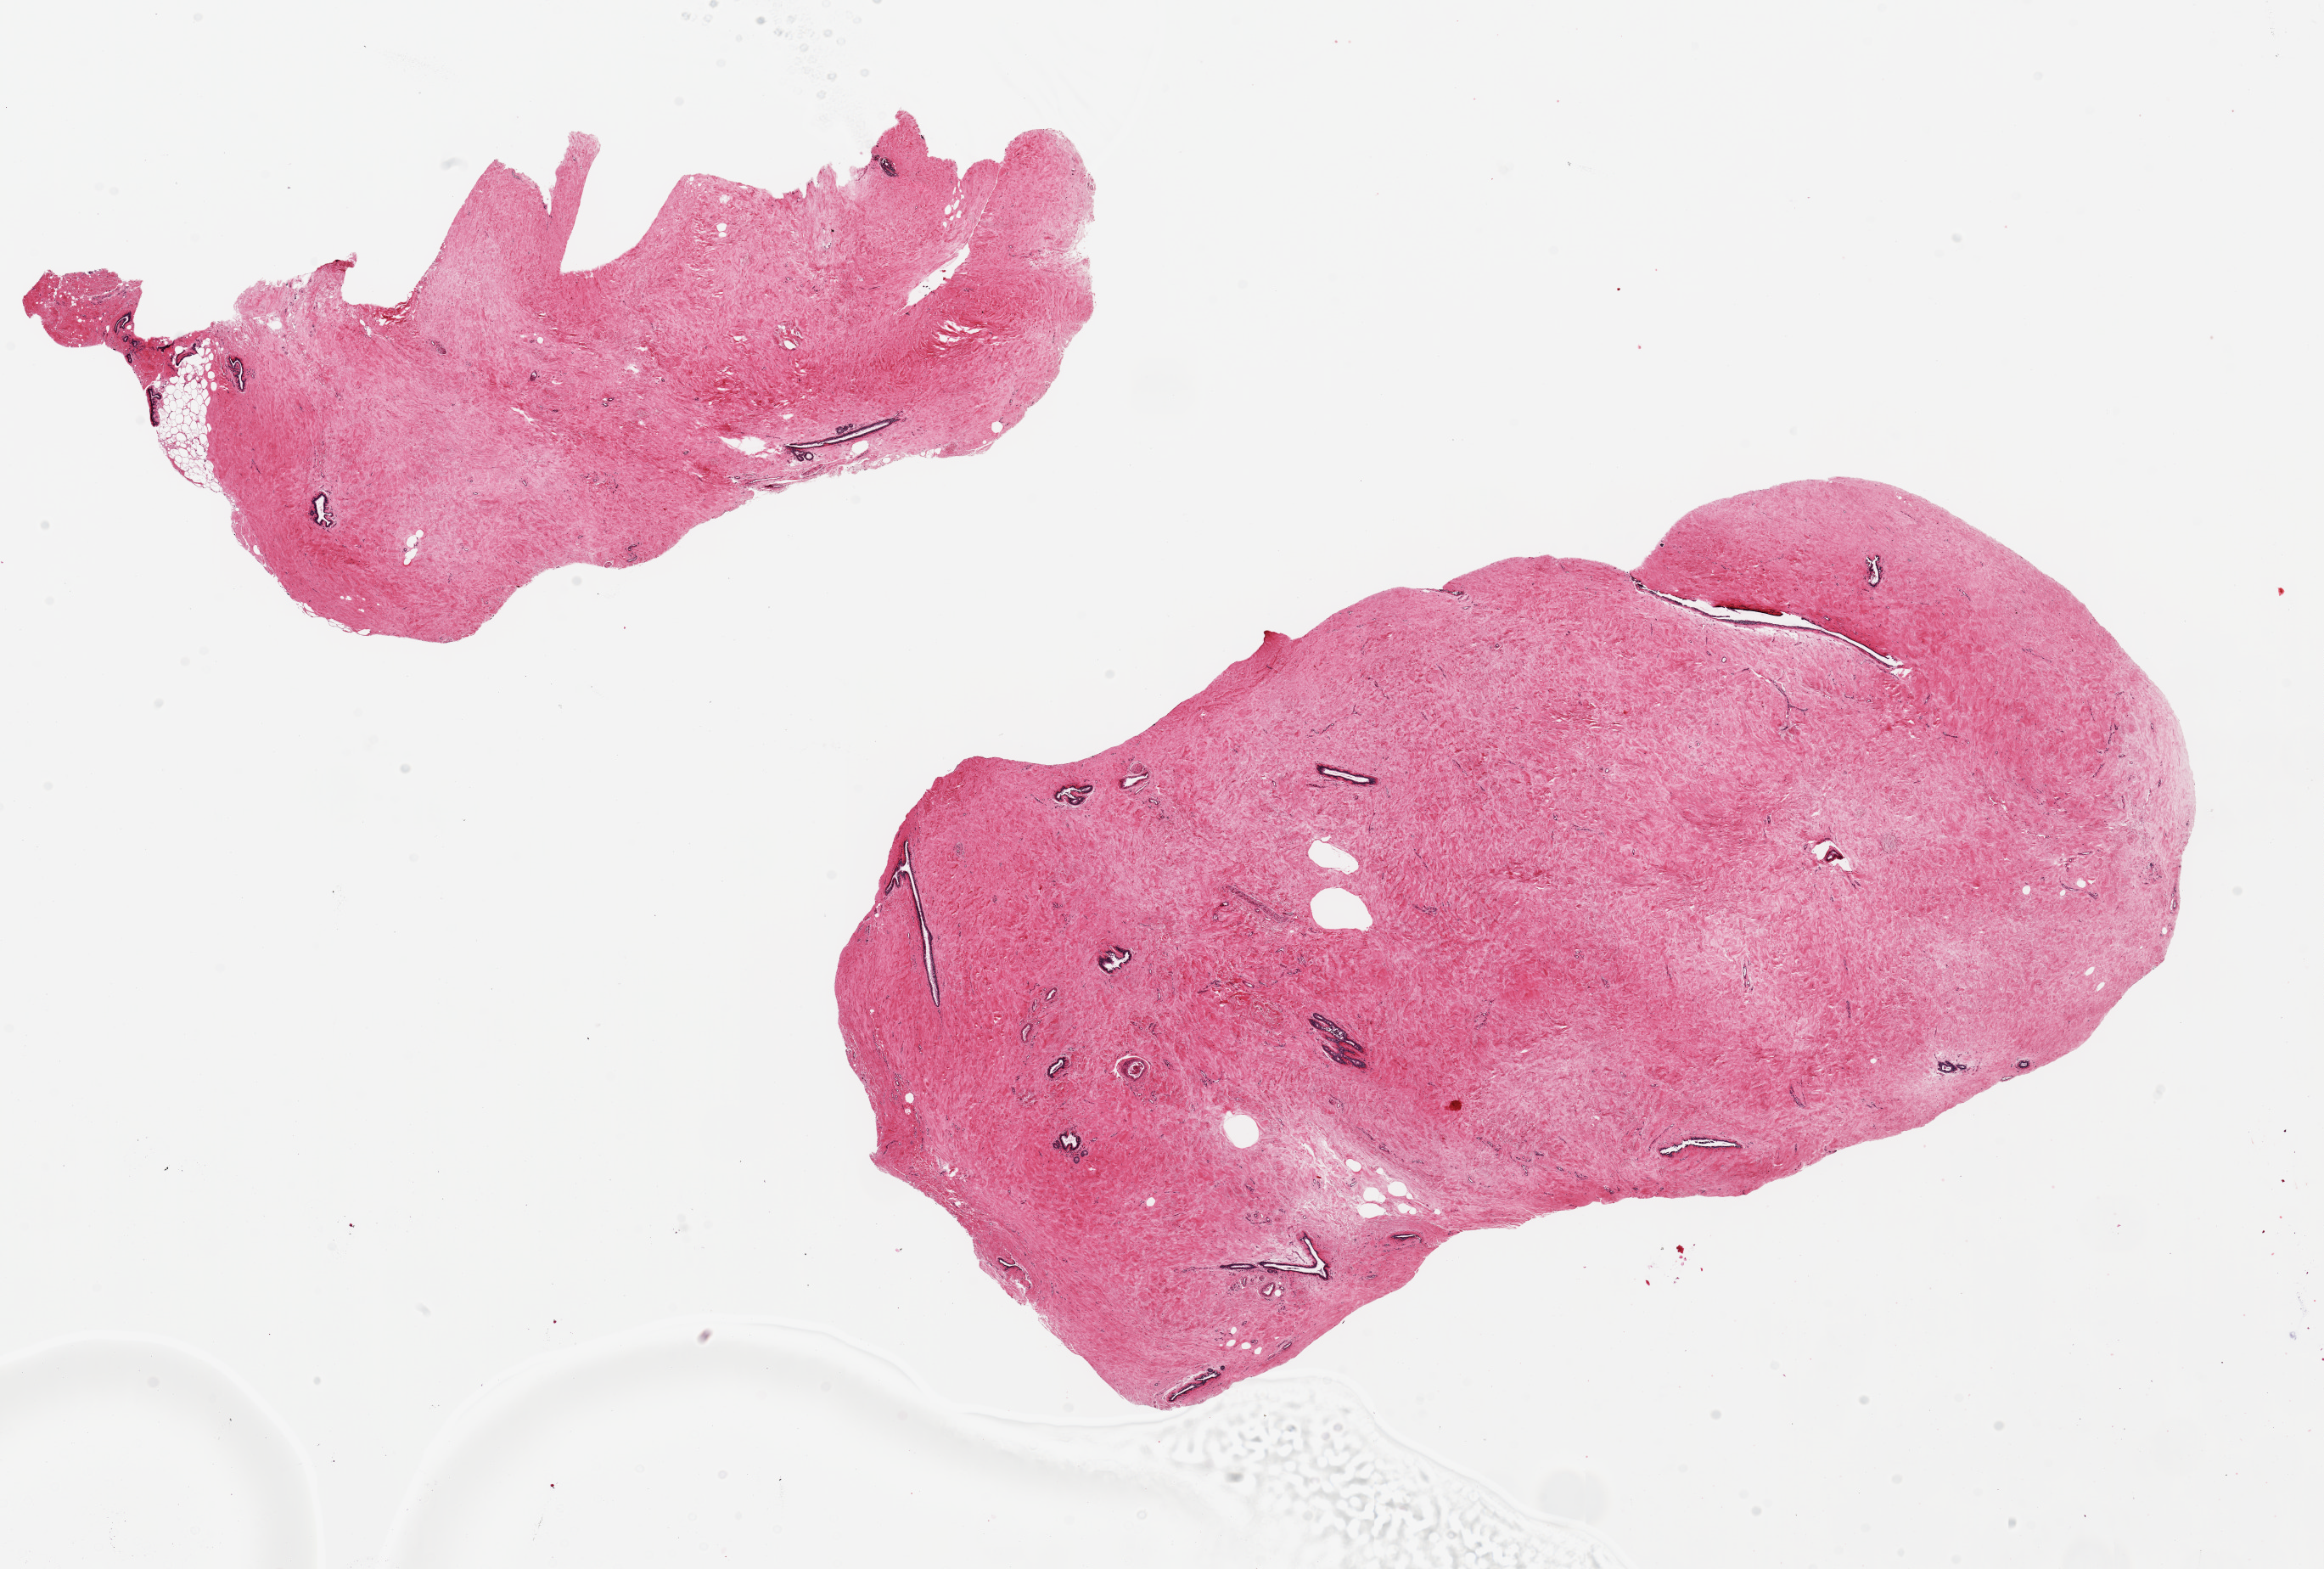
Haematoxylin and eosin whole-slide image, brightfield, a low-resolution overview of the entire scanned area, about 21.7 x 14.6 mm; PAXgene-fixed, paraffin-embedded tissue; target tissue: breast; tissue donor sample. Male donor.
Pathologist's review note for this sample: 2 pieces ~12x6.5&8.3x3.8 mm Gynecomastia: fibrous stroma and ducts; ~2% fat.